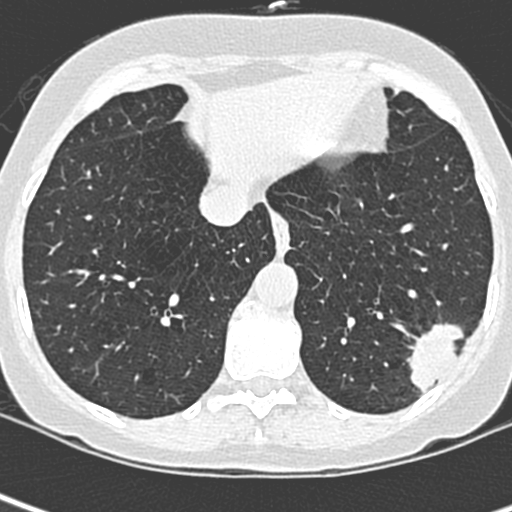
Low-dose screening chest CT, one axial slice. Slice 79 of 252 in the series (ordered by position). 120 kVp. Lung window (W 1500 / L -600 HU). 1.3 mm slice thickness. 512 × 512 image matrix.
Structures marked on this image (manually delineated by an expert):
- lesion 1 (tumor, lower lobe of left lung): bounding box (x1, y1, x2, y2) in pixels: (406, 323, 464, 394)